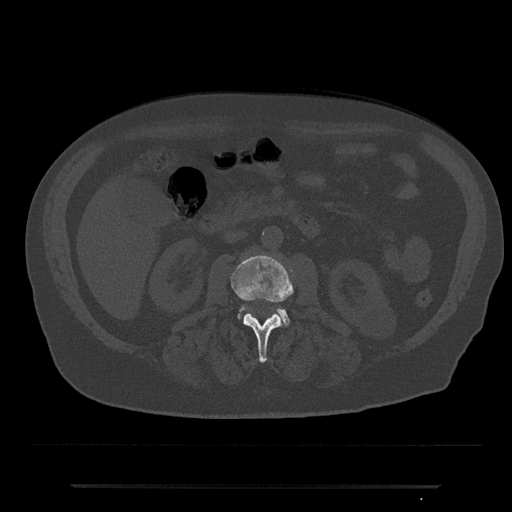
CT including the spine, one axial slice. Position 452 of 797 along the scan axis. Reconstruction kernel Br40s/3. 120 kVp. Bone window (W 1800 / L 400 HU). 0.5 mm slice thickness. 512 × 512 image matrix, field of view 434 × 434 mm. Patient: male, 80 years. From the clinical record (not read from this slice): primary cancer: prostate; vertebrae with lytic lesions (as recorded): L1, T11.
Annotated regions visible in this slice (semi-automatically segmented with operator editing):
- L2 vertebra: bounding box [x1, y1, x2, y2] px = [231, 255, 293, 363]
- L3 vertebra: [237, 307, 291, 326]